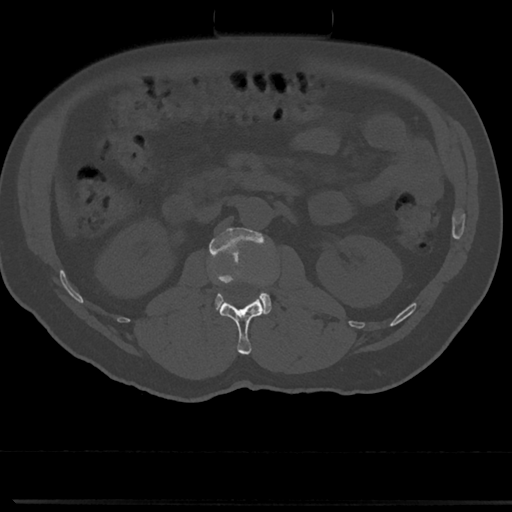
CT including the spine, one axial slice. Position 48 of 817 along the scan axis. 120 kVp. Bone window (W 1800 / L 400 HU). 512 × 512 image matrix, field of view 355 × 355 mm. Patient: male, 61 years. From the clinical record (not read from this slice): primary cancer: prostate.
Structures marked on this image (semi-automatically segmented with operator editing):
- L1 vertebra: box from (x=219, y=297) to (x=264, y=355) px
- L2 vertebra: (x=209, y=227)–(x=272, y=315)